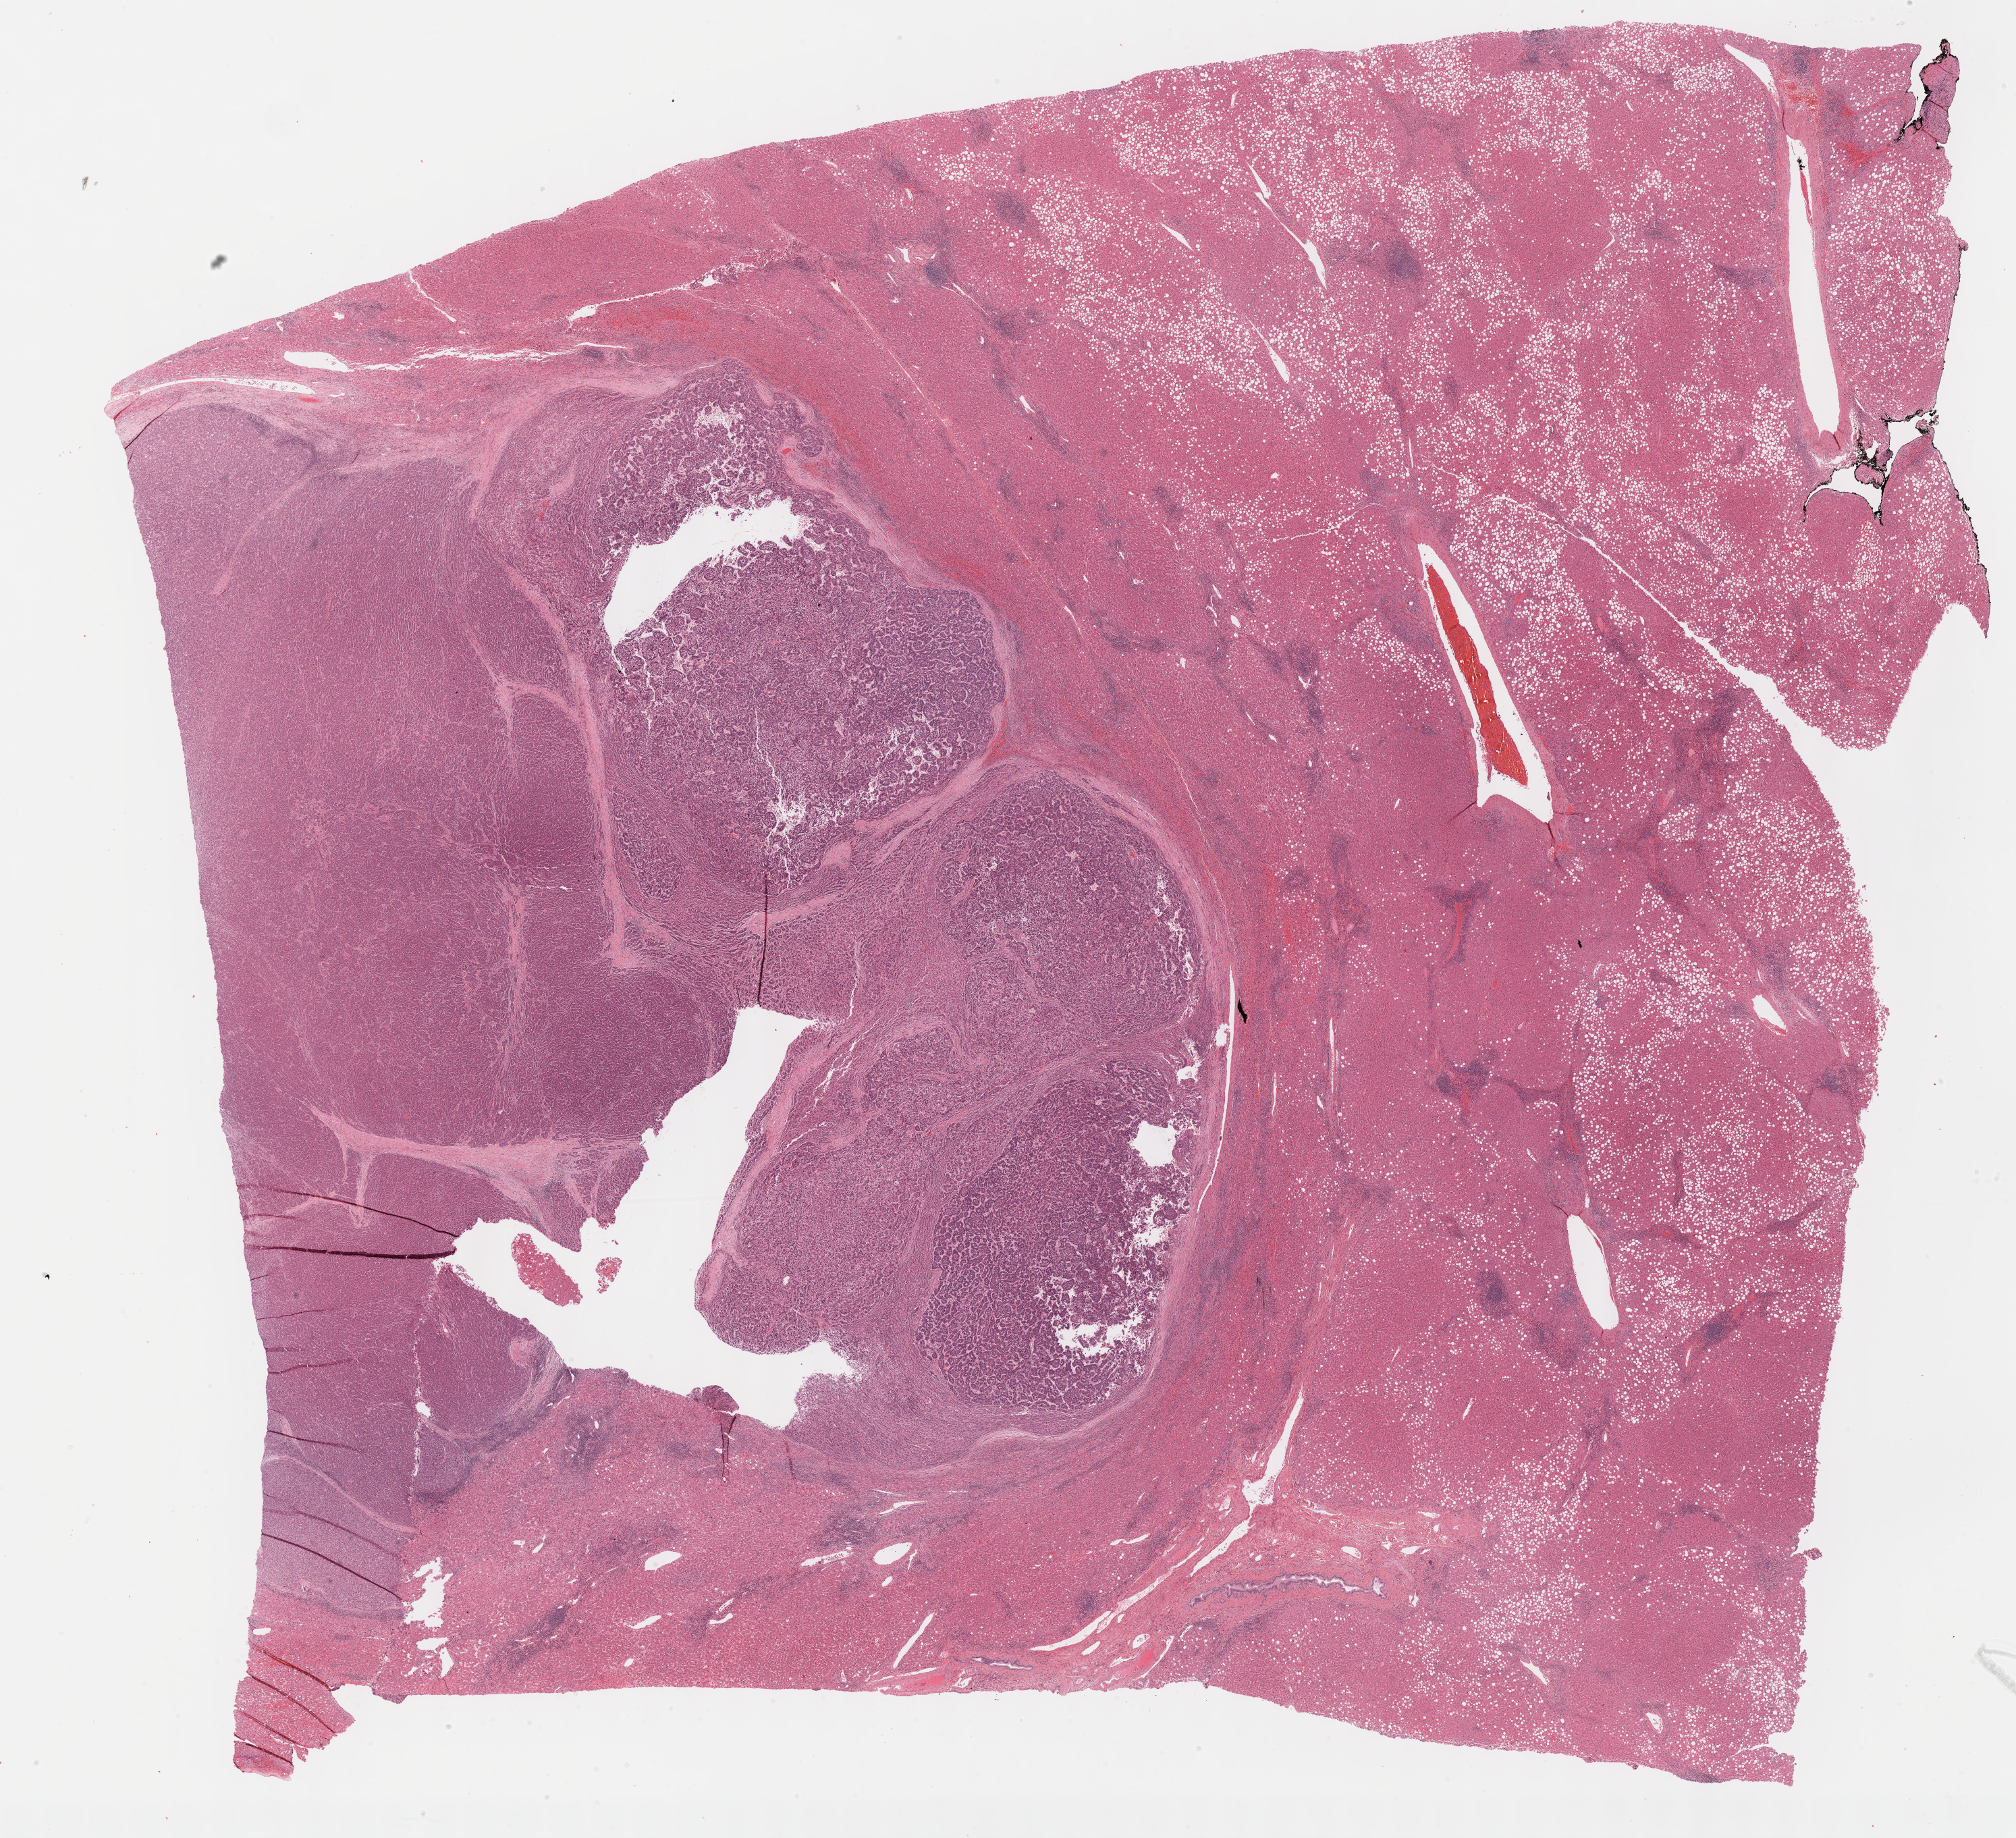
Digitized H&E tissue section (whole slide), a low-resolution overview of the entire scanned area, about 24.2 x 22.0 mm; FFPE section; primary tumour sample from the liver. Female, age 52 years at initial diagnosis.
Pathologic diagnosis: Hepatocellular carcinoma, NOS.